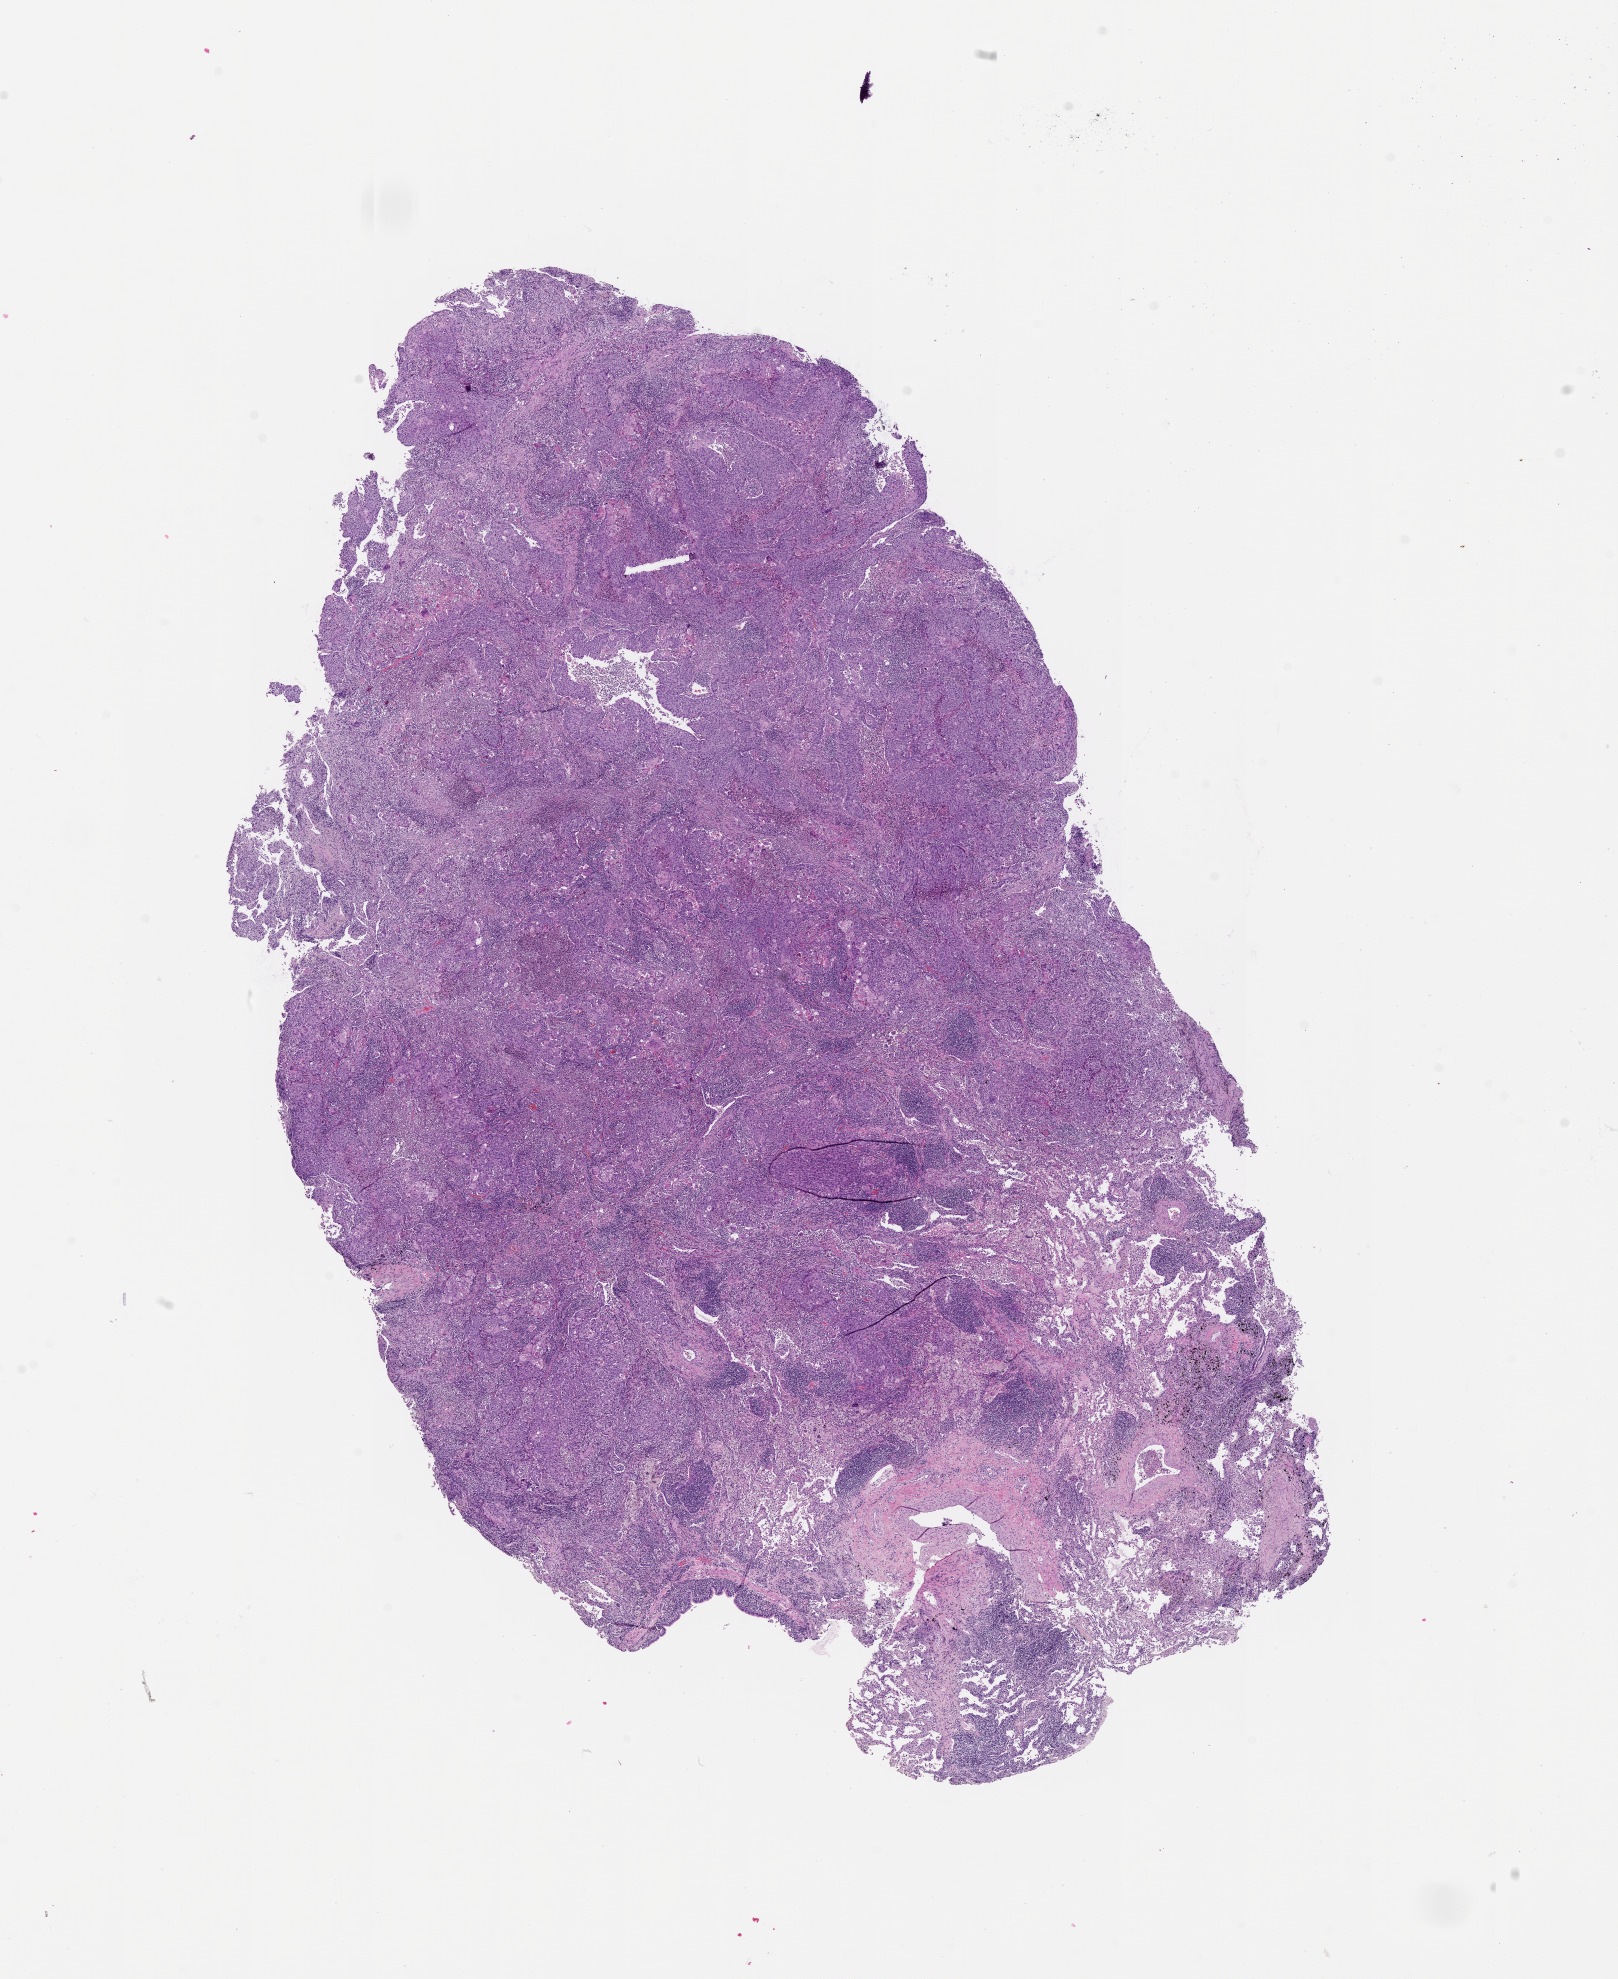
Digitized H&E-stained tissue section (whole slide) — low-resolution overview of the scanned area, about 13.0 x 15.9 mm; tumour tissue sample, lung. 64-year-old male patient.
Patient diagnosis (cohort enrolment): squamous cell carcinoma (lung).